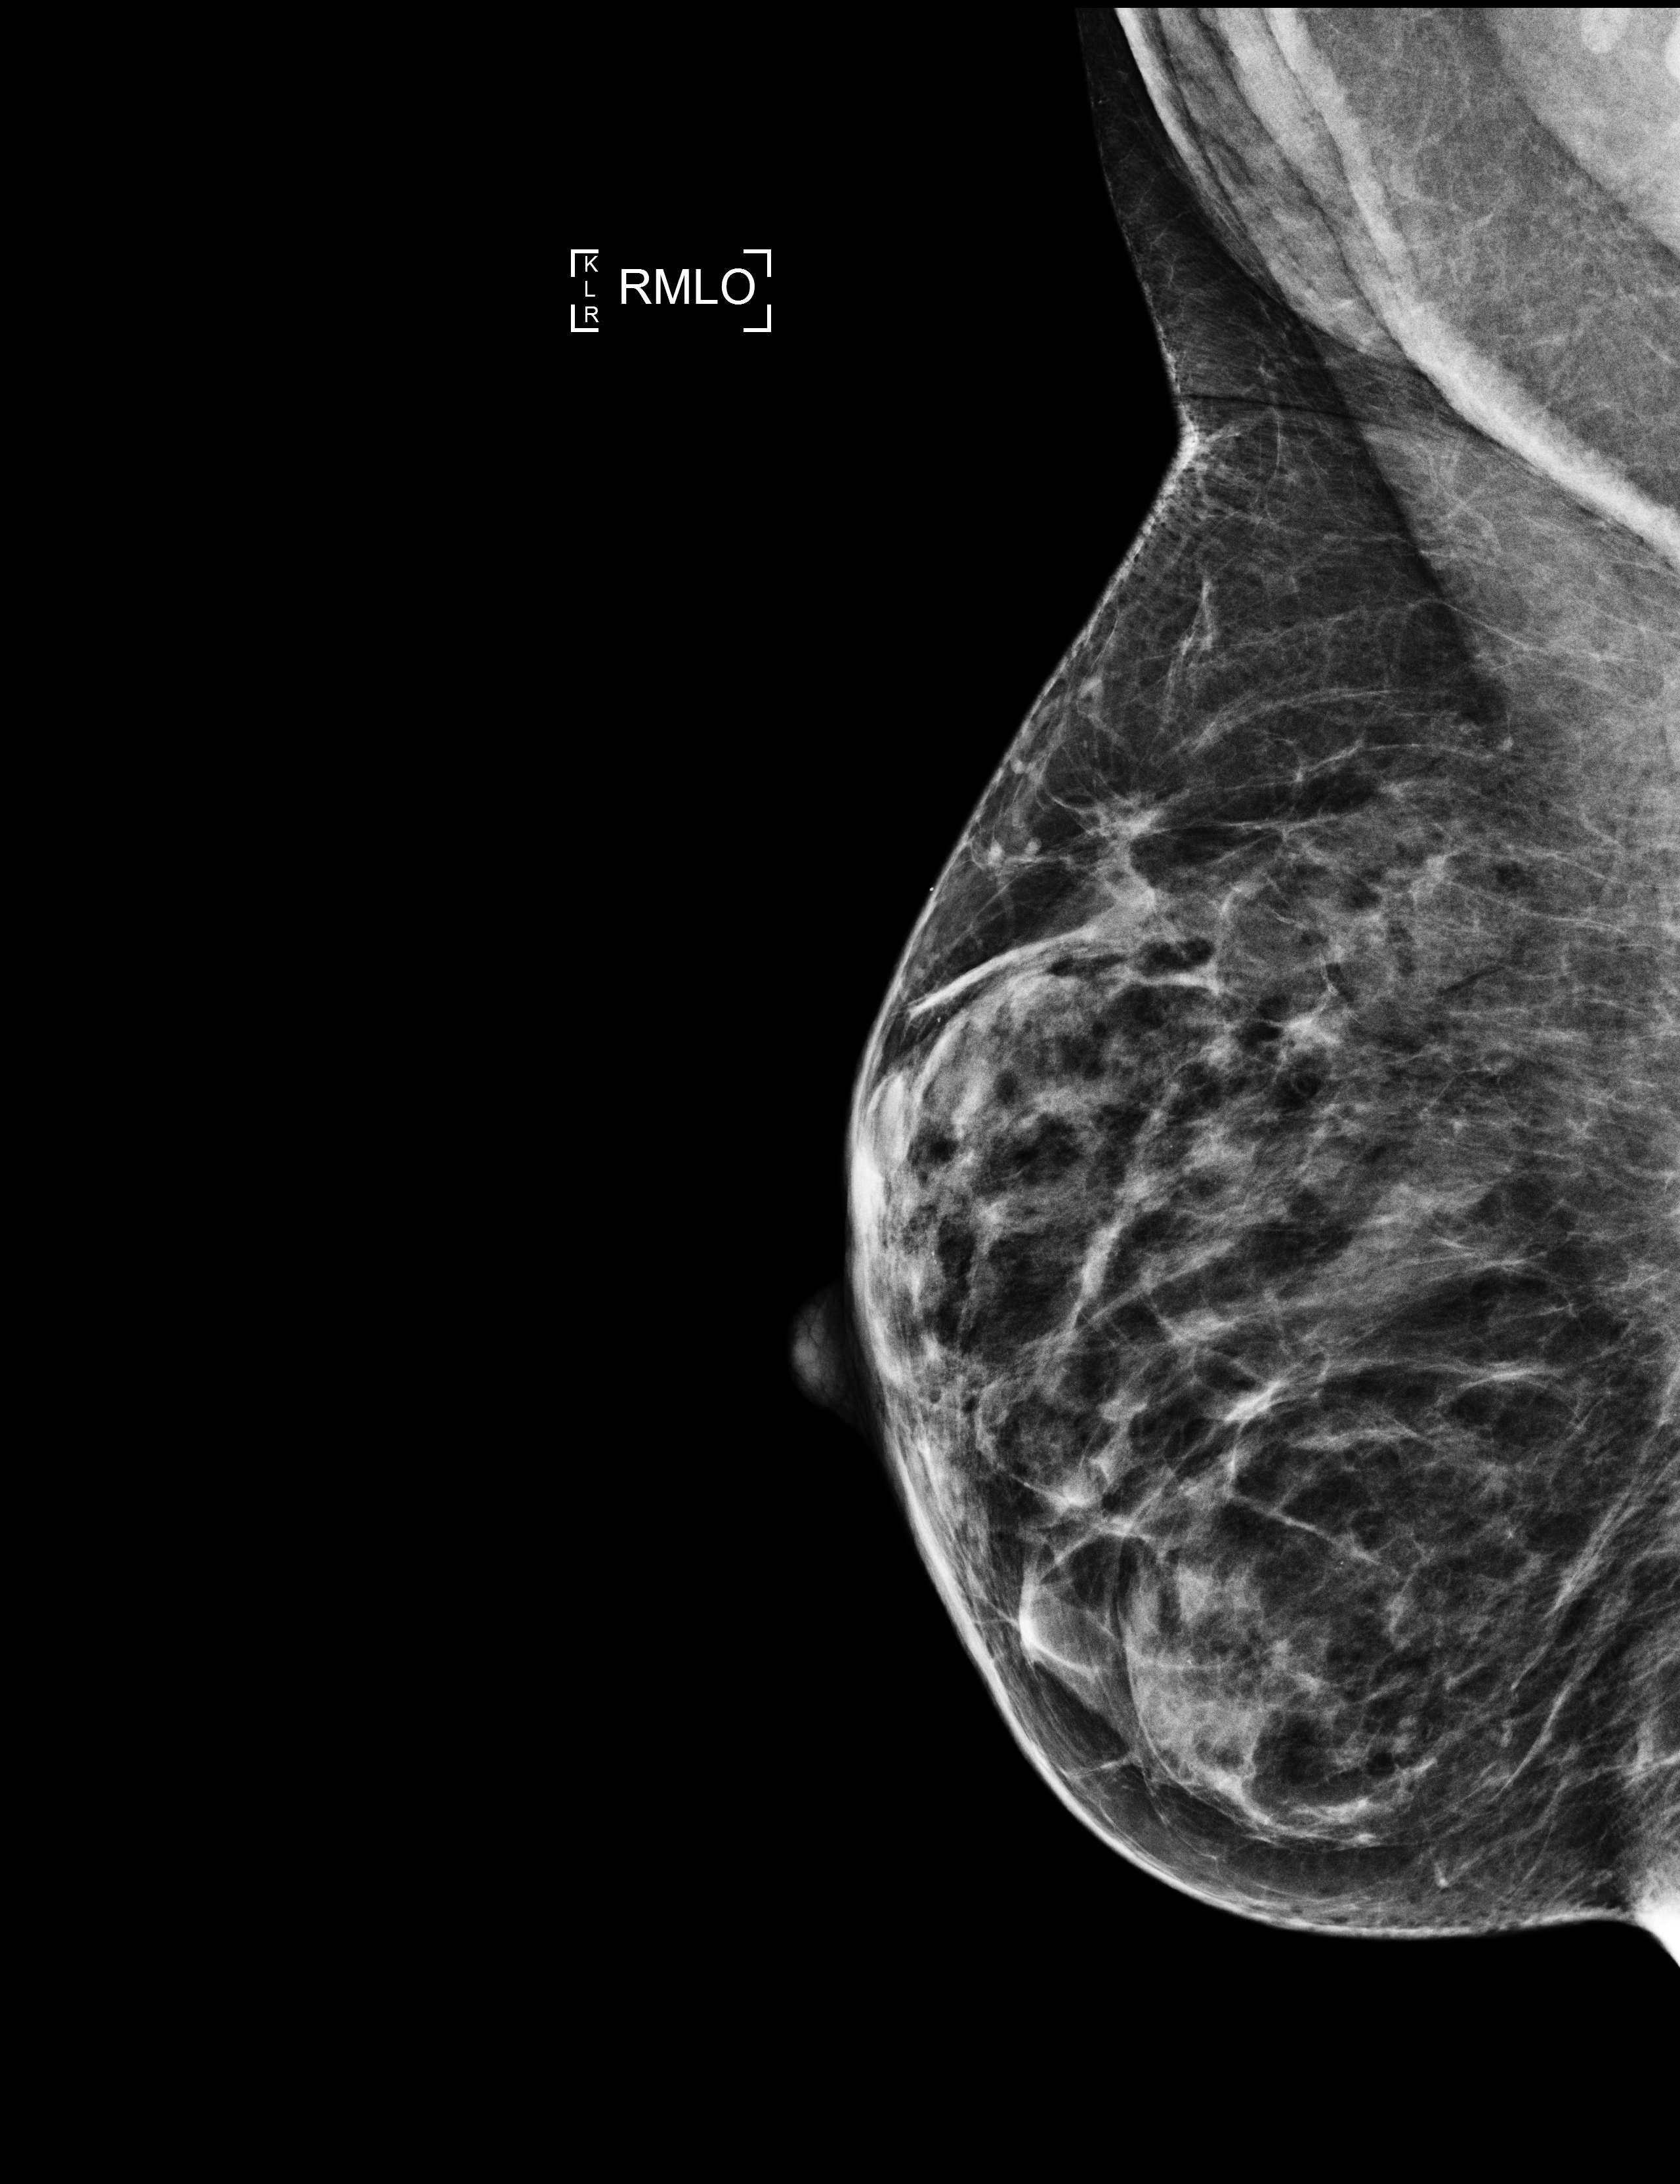
Annual screening mammography examination; compressed breast thickness 41 mm; system: Selenia Dimensions. Female patient, age 62 years.
Image type: full-field digital mammogram. Breast: right. Projection: mediolateral oblique (MLO) view.